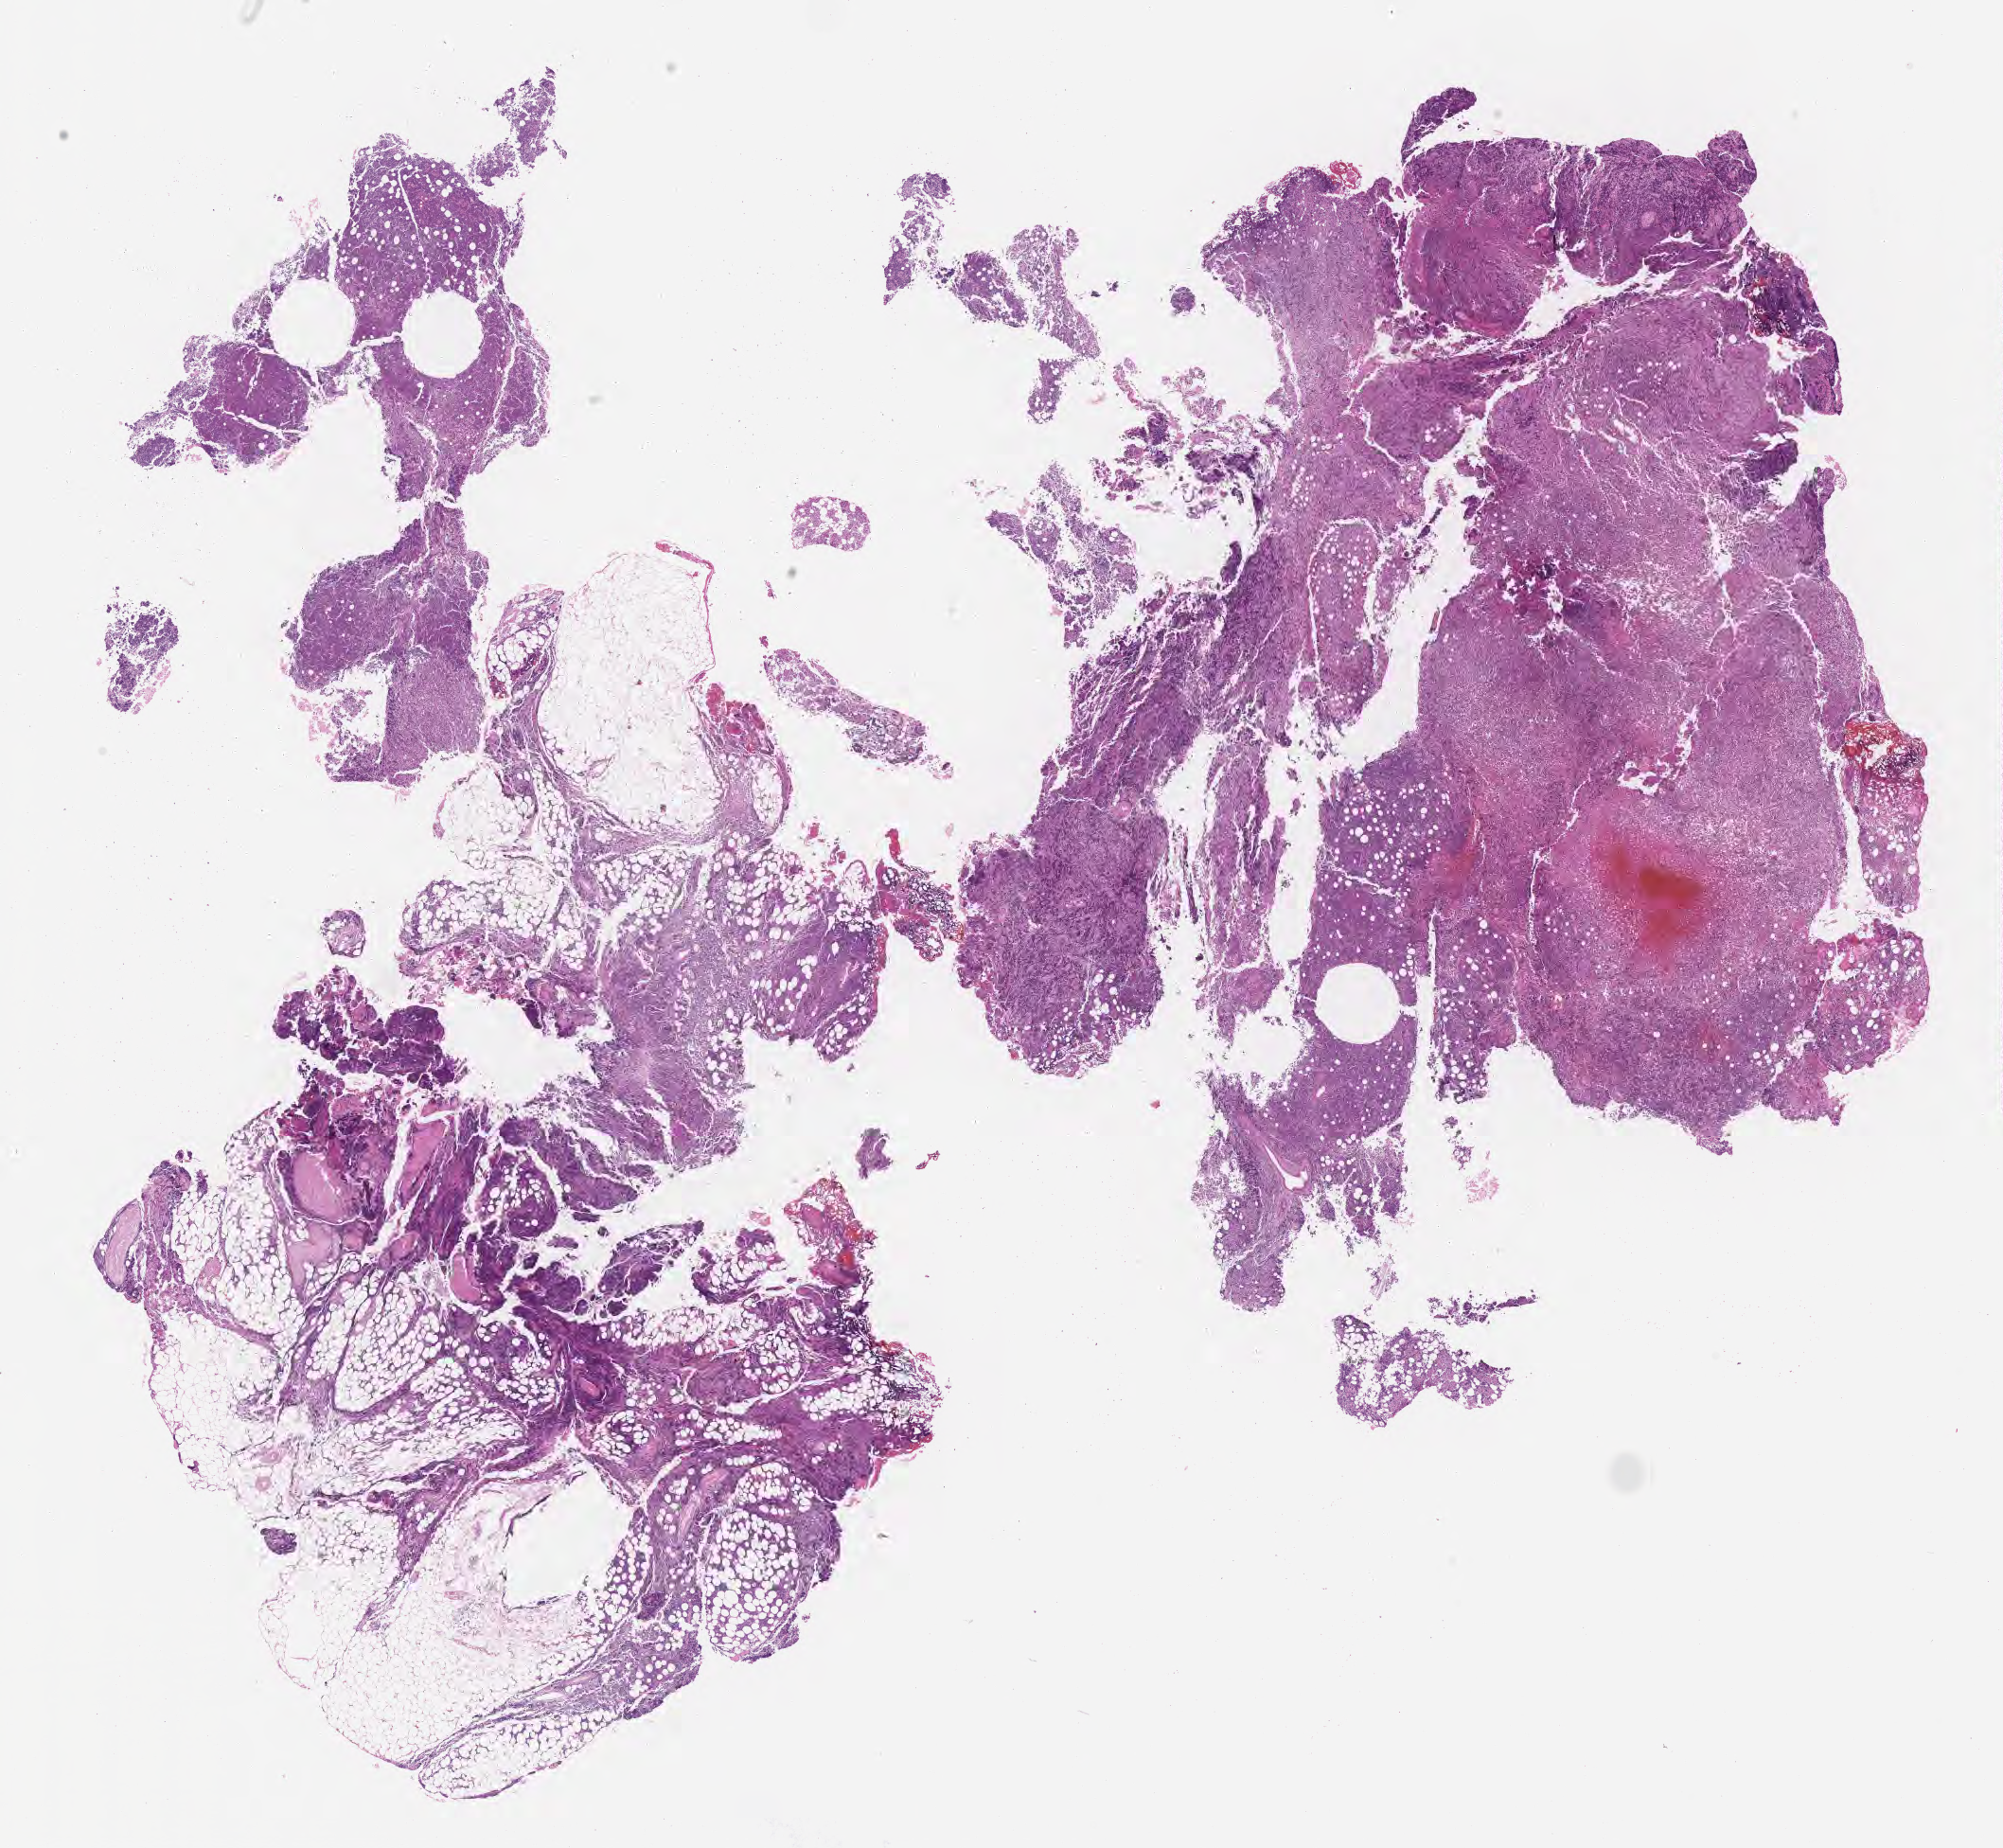
Whole-slide image, haematoxylin and eosin stain, a low-resolution overview of the entire scanned area, about 17.1 x 15.8 mm, FFPE section, primary tumor. Female patient, aged 70. Slide review estimates, as recorded: tumor cells 80%, tumor nuclei 90%, stromal cells 10%, necrosis 5%, normal cells 5%. Infiltration values recorded for this section: lymphocyte infiltration 50%, monocyte infiltration 20%, neutrophil infiltration 10%.
* Ann Arbor stage (patient): Stage II
* section: top of the tissue portion
* diagnosis: Burkitt lymphoma, NOS